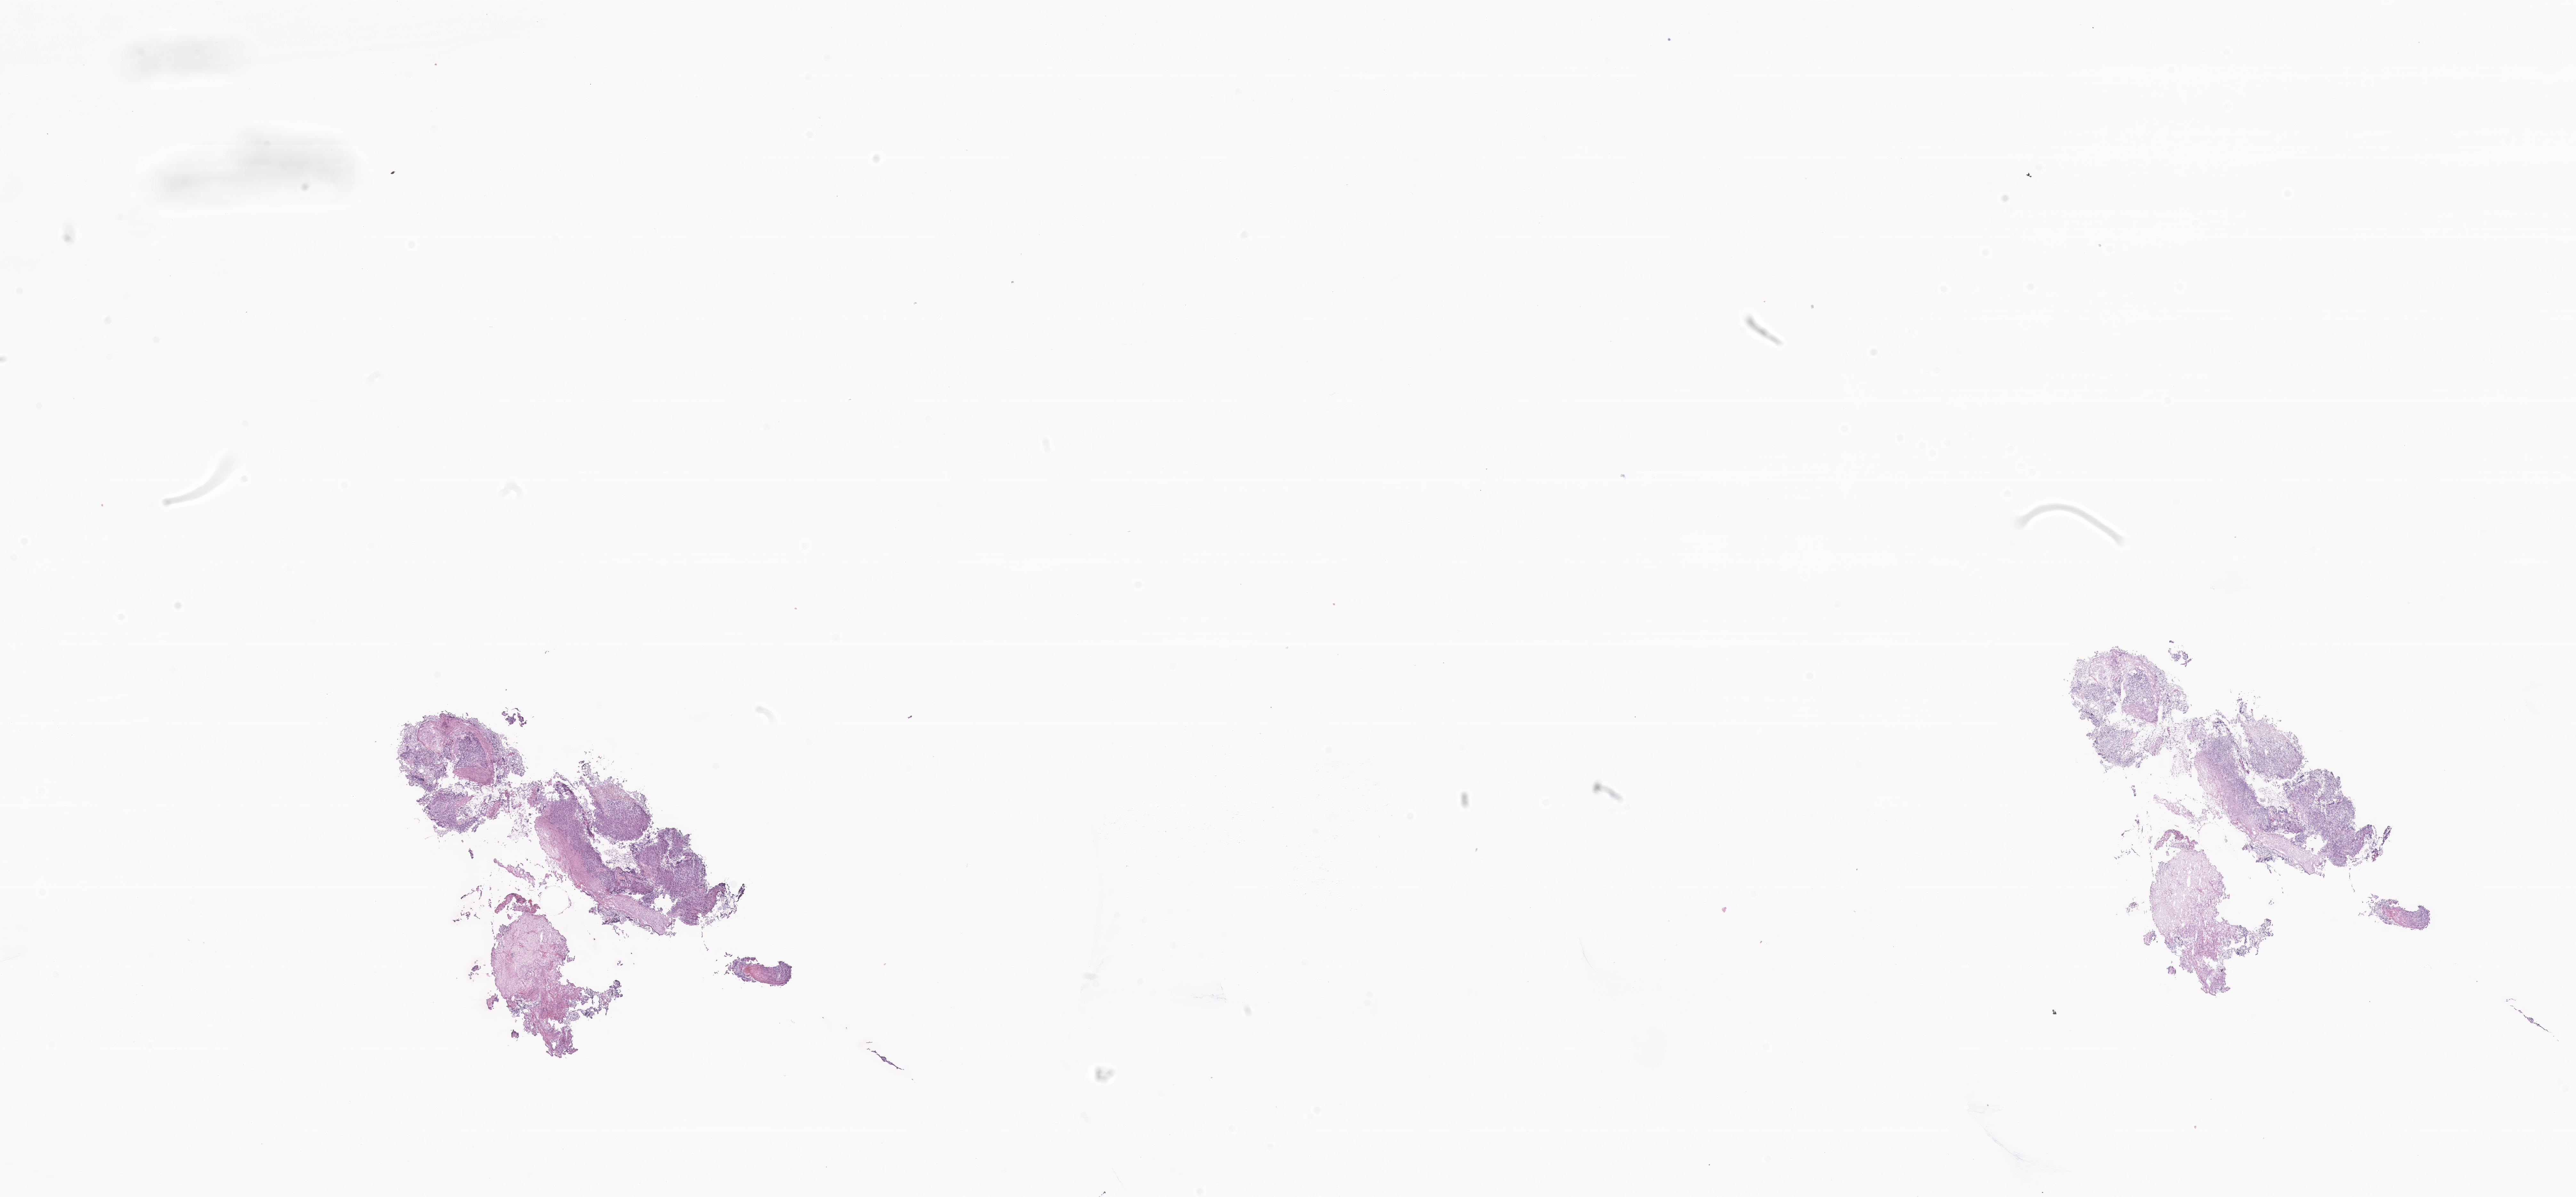
Whole-slide image, haematoxylin and eosin stain of tumor tissue from the brain — low-resolution overview of the scanned area, about 33.9 x 15.8 mm. Frozen section. Patient female; age 63 months (5 years 3 months).
* recorded diagnosis: Medulloblastoma, NOS